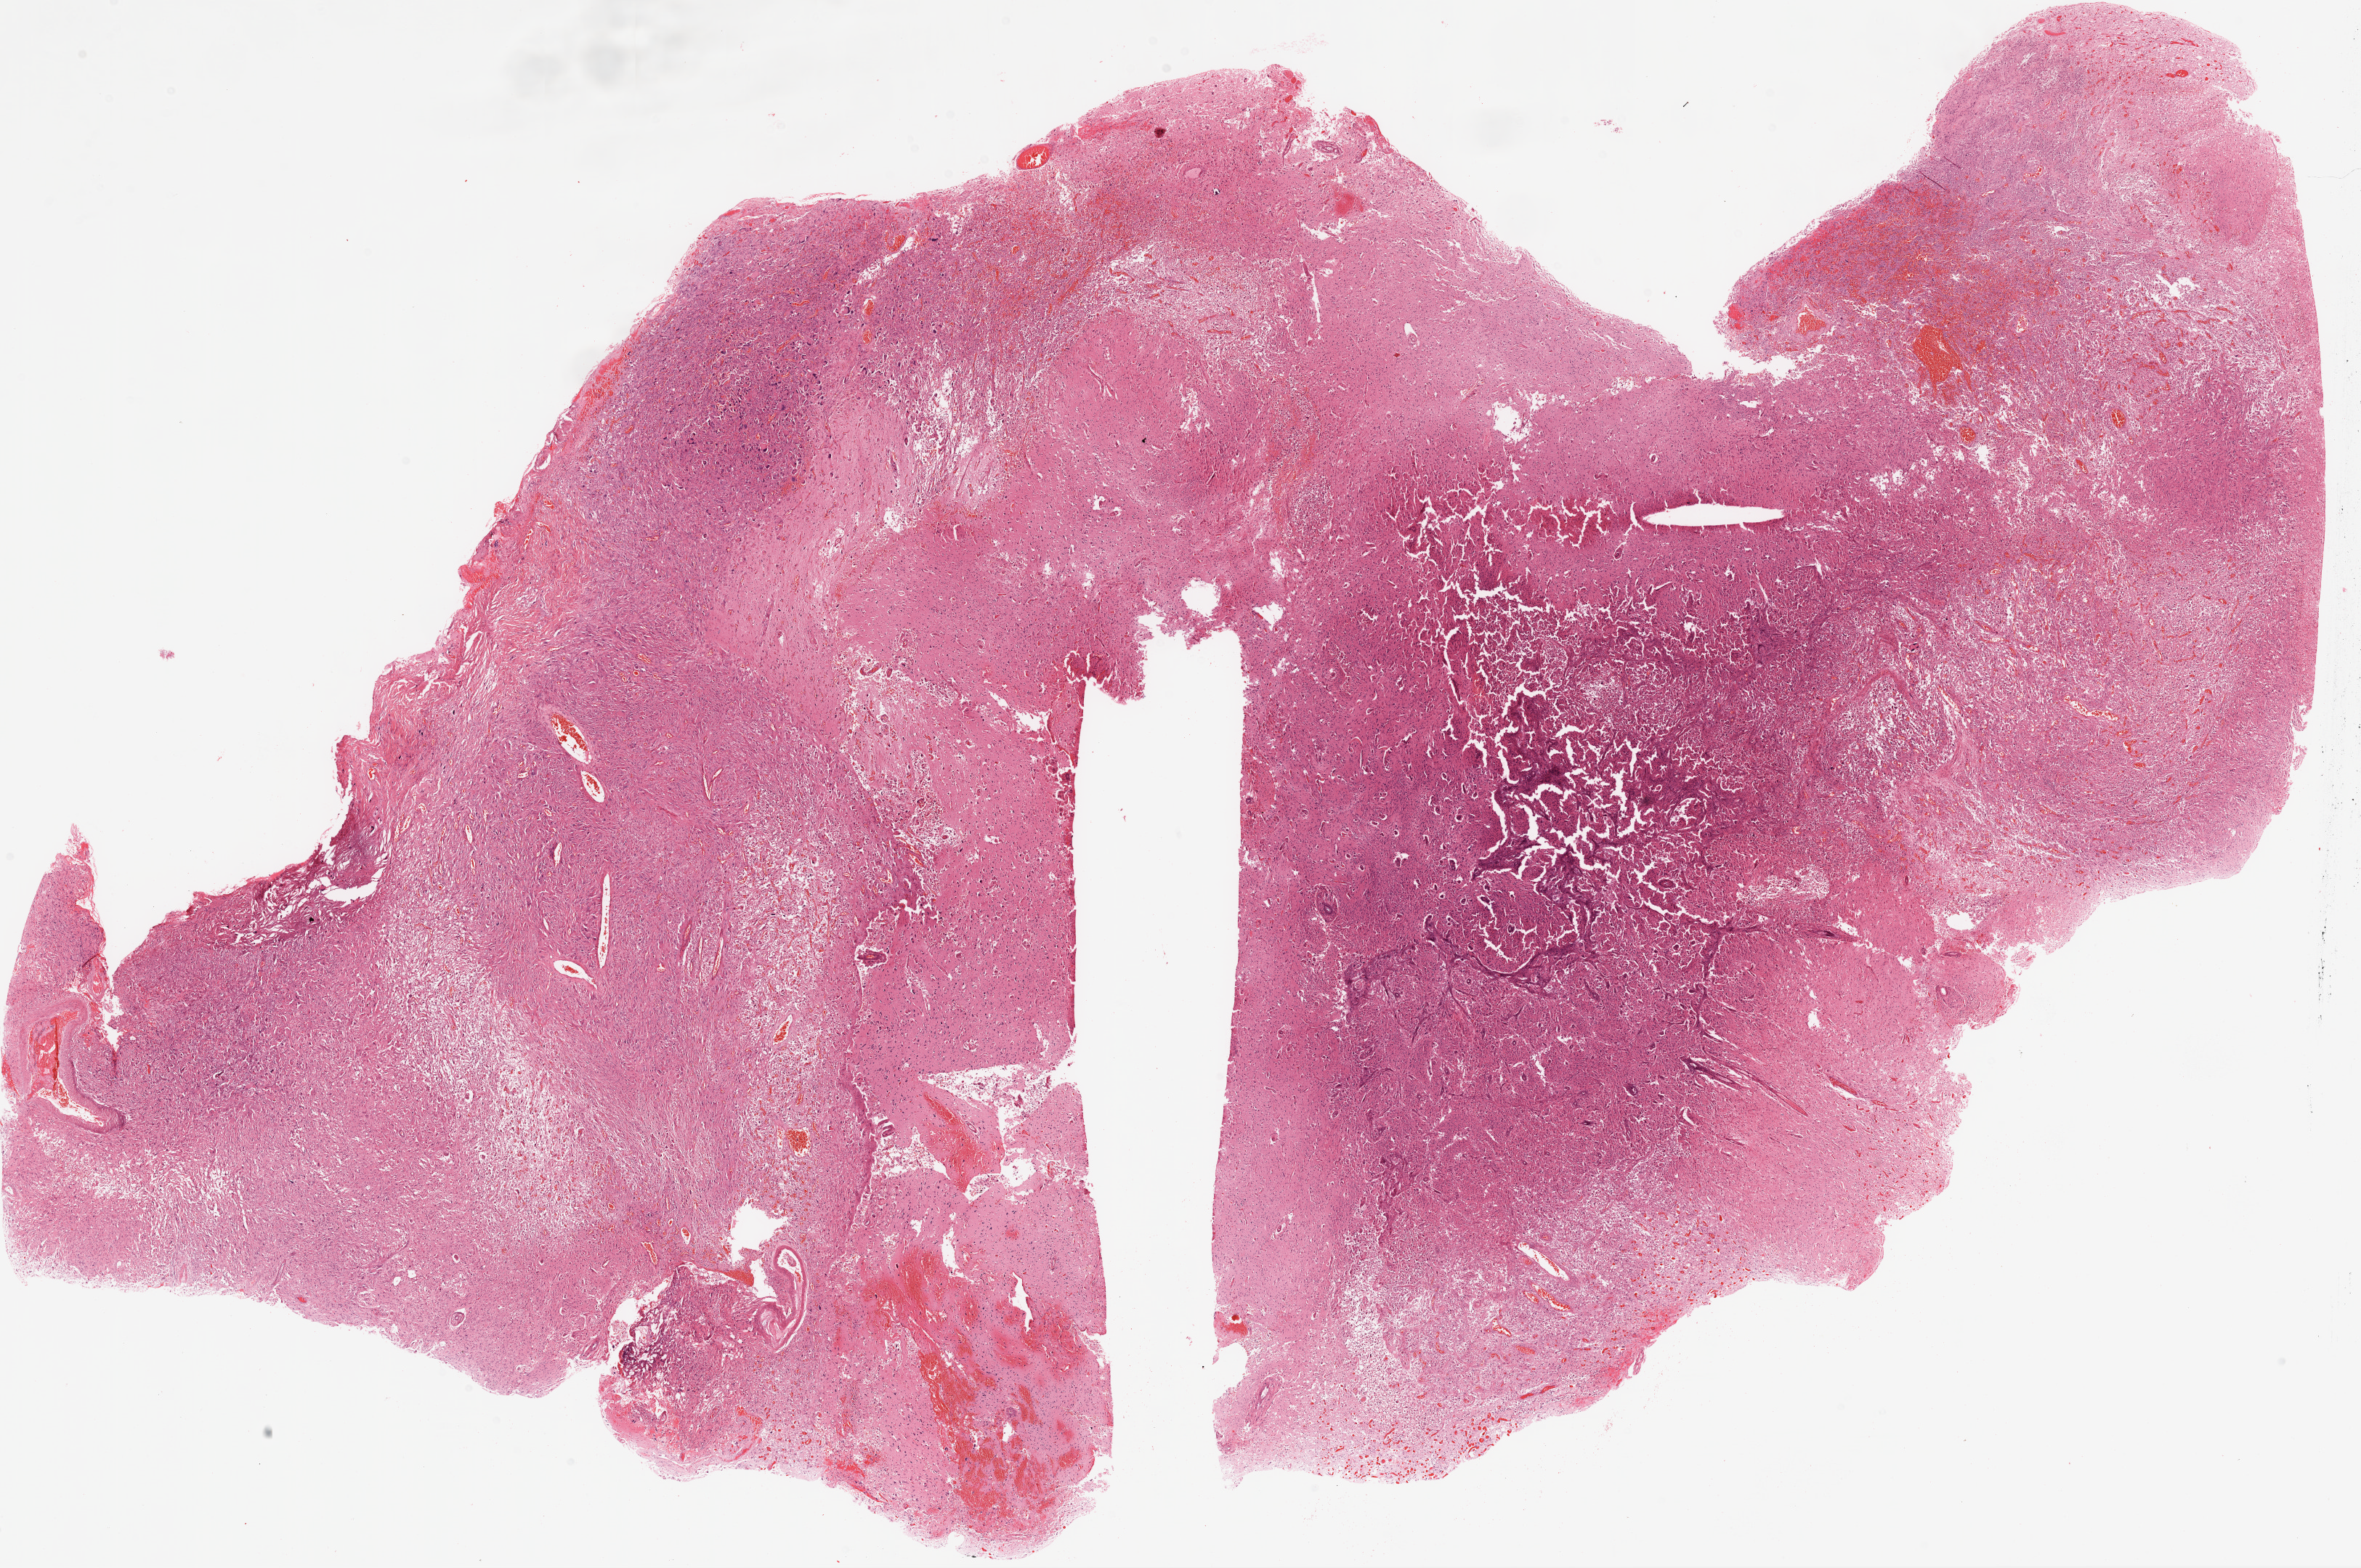
Whole-slide histology image, H&E, whole scanned area (about 26.1 x 17.3 mm, slide scanned at 20x) shown as a low-resolution overview. Formalin-fixed paraffin-embedded (FFPE) diagnostic section. Brain, primary tumour sample. Patient: female, age at initial diagnosis 44 years.
Histologic diagnosis: Glioblastoma.